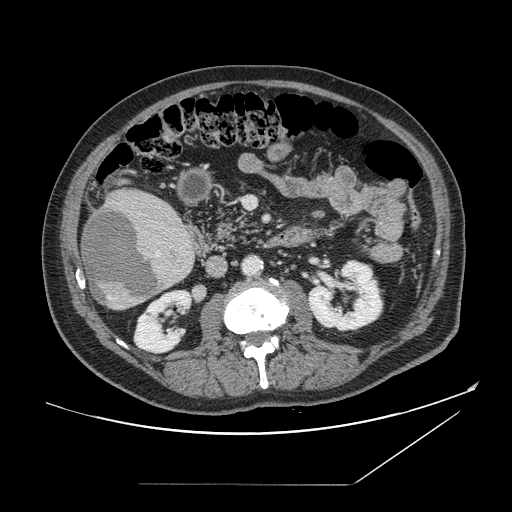
Contrast-enhanced abdominal CT, one axial slice. 120 kVp. Soft-tissue window (W 400 / L 40 HU). 512 × 512 image matrix, field of view 416 × 416 mm. Male patient, age 80 years. Case-level facts recorded for this patient, not image findings: diagnosis: colorectal cancer liver metastases, imaged before liver resection; multiple liver metastases: no; largest metastasis: 2.2 cm; disease in both lobes: no.
Outlined on this slice (outlined manually by an expert reader):
- liver: box from (x=81, y=190) to (x=196, y=310) px
- planned liver remnant (the part of the liver to remain after resection): (x=136, y=192)–(x=167, y=207)
- liver metastasis: (x=85, y=208)–(x=163, y=304)